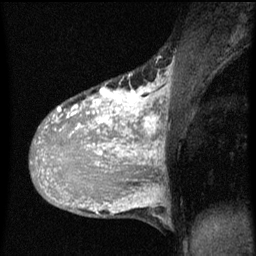
Breast MRI (dynamic contrast-enhanced), one sagittal slice; slice 31 of 60 in the series (ordered by position); dynamic contrast-enhanced series, image 2 of 3 at this slice position (ordered by acquisition); 1.5 T; TE 4.2 ms, TR 8 ms; 2 mm slice thickness; 256 × 256 image matrix, field of view 180 × 180 mm. Female patient, age 36 years.
Annotated regions visible in this slice (semi-automatic segmentation, software-assisted and operator-edited):
- analysis volume of interest (the breast-tissue region the enhancement analysis was run in; not a lesion): bounding box (x1, y1, x2, y2) in pixels: (32, 80, 167, 161)
- tumour enhancement mask (voxels above the 70 % enhancement threshold inside the analysis volume of interest): (36, 80, 167, 161)